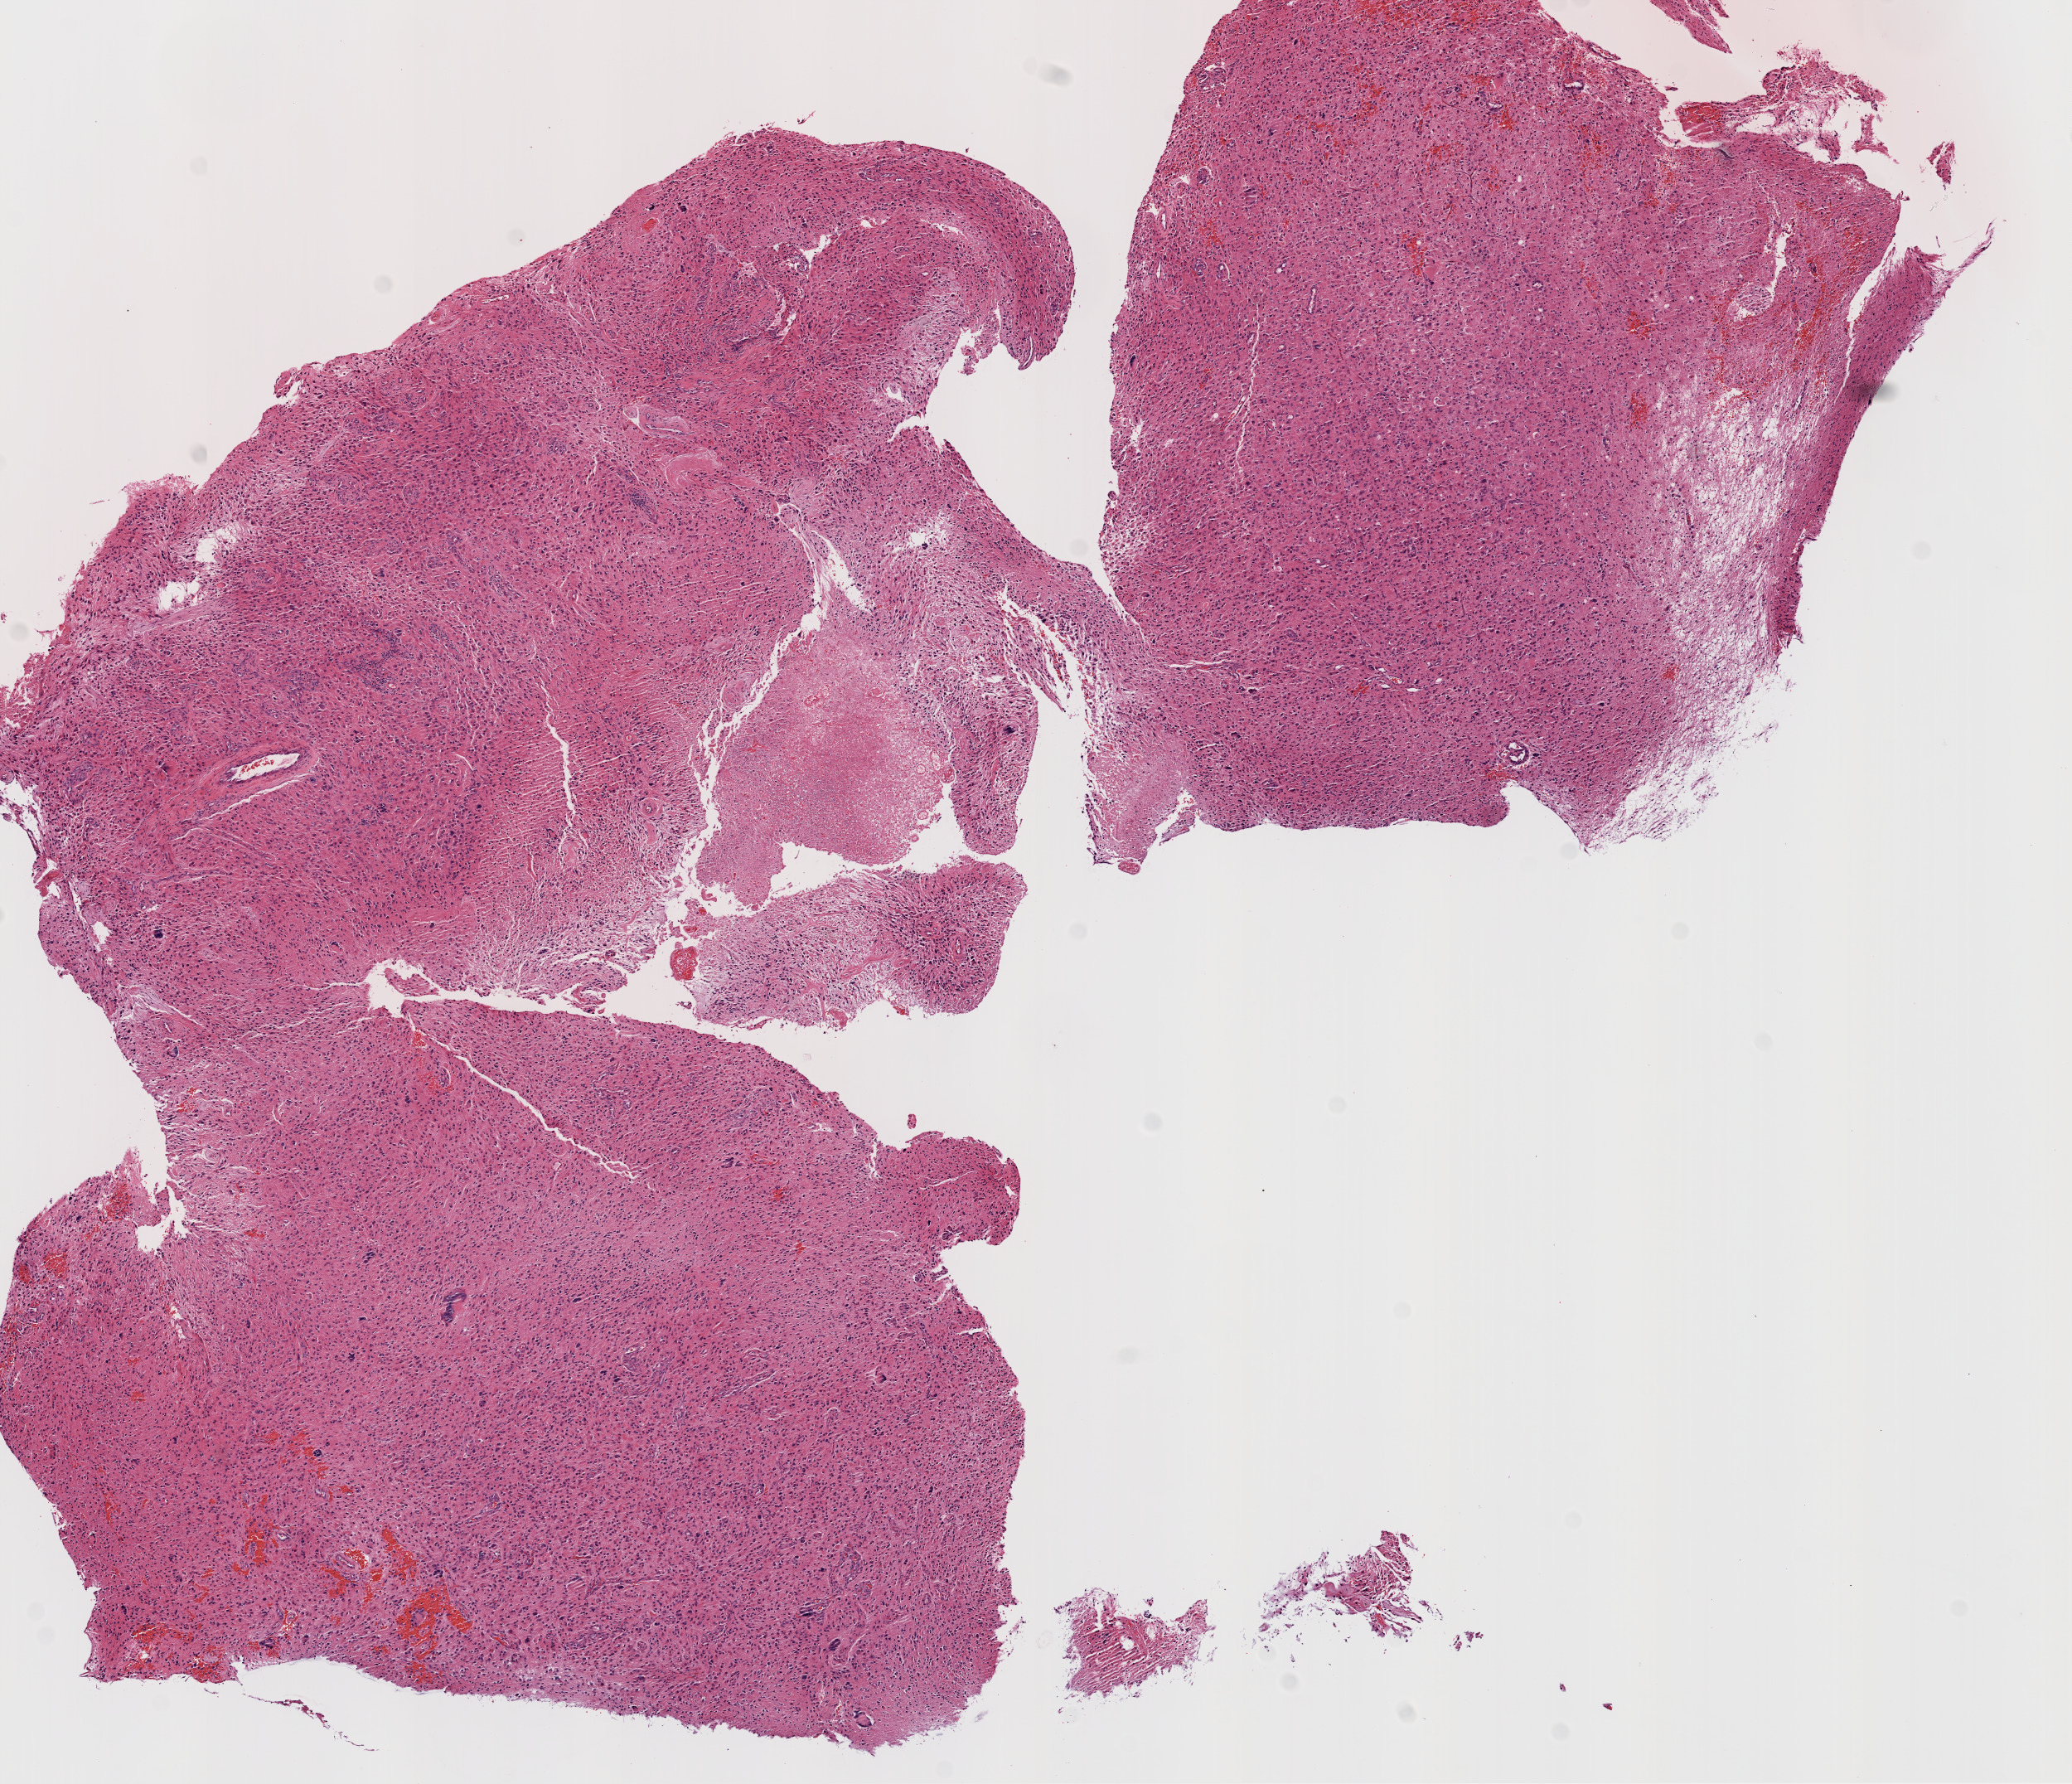
Digitized Hematoxylin and eosin (H&E) stained tissue section (whole slide), a low-resolution overview of the entire scanned area, about 10.0 x 8.6 mm (from a 20x scan), FFPE section, brain, primary tumour sample. Male patient; age at initial diagnosis 69 years.
Pathologic diagnosis: Glioblastoma.